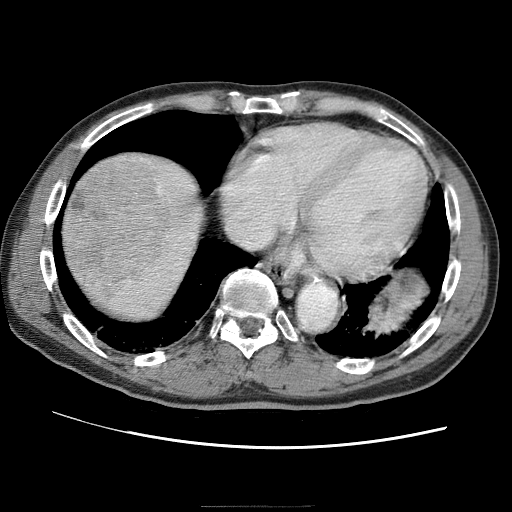
Contrast-enhanced abdominal CT (liver protocol), one axial slice. Position 64 of 75 along the scan axis. 120 kVp. One of 2 acquisitions stored at this slice position. Soft-tissue window (W 400 / L 40 HU). 2.5 mm slice thickness. 512 × 512 image matrix, field of view 360 × 360 mm. Case-level facts recorded for this patient, not image findings: diagnosis: hepatocellular carcinoma (patient treated with transarterial chemoembolisation; whether this scan precedes or follows treatment is not stated here); TNM stage (as recorded): Stage-II; Child-Pugh class: A; tumour differentiation: well differentiated; tumour nodularity: multinodular.
Structures marked on this image (semi-automatically segmented with operator editing):
- liver parenchyma outside the tumour (the mass and vessels are separate outlines, so this box may not span the whole liver): bounding box <60,148,210,324> (left, top, right, bottom; pixels)
- mass: <63,154,174,293>
- liver vessels: <126,152,194,272>